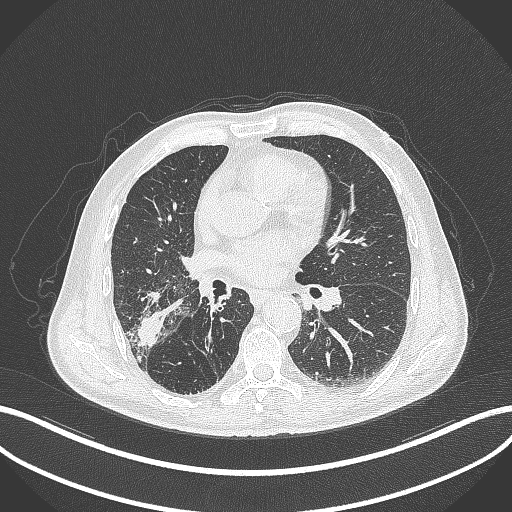
Chest CT, one axial slice. Position 210 of 429 along the scan axis. 120 kVp. Lung window (W 1500 / L -600 HU). 1 mm slice thickness. 512 × 512 image matrix. Patient: male, 72 years. From the clinical record (not read from this slice): clinical TNM (as recorded): T3 N2 M0.
Annotated regions visible in this slice (rectangle marked by the reading radiologist):
- lung tumour (recorded histology: adenocarcinoma): bounding box <133,311,167,350> (left, top, right, bottom; pixels)